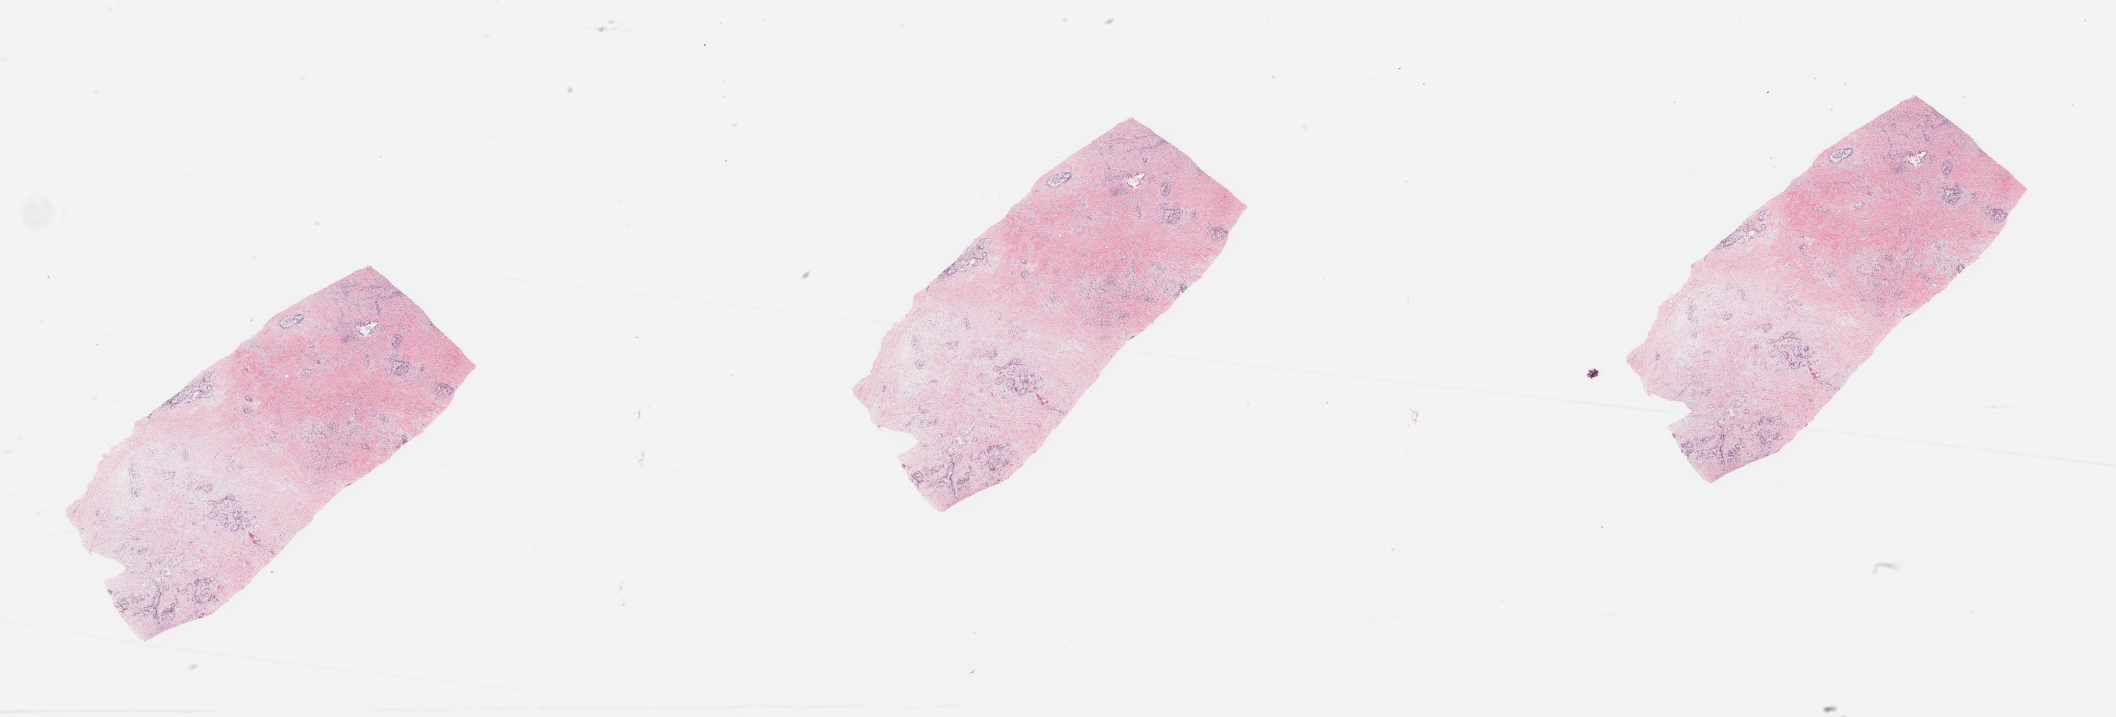
H&E whole-slide image — whole scanned area (about 33.5 x 11.3 mm, from a 20x scan) shown as a low-resolution overview. Pancreas, tumour tissue. 63-year-old male patient. Histologic grade: G2 (moderately differentiated).
Diagnosis: Infiltrating duct carcinoma, NOS. Primary tumour site (as recorded): tail. AJCC pathologic stage: IB.